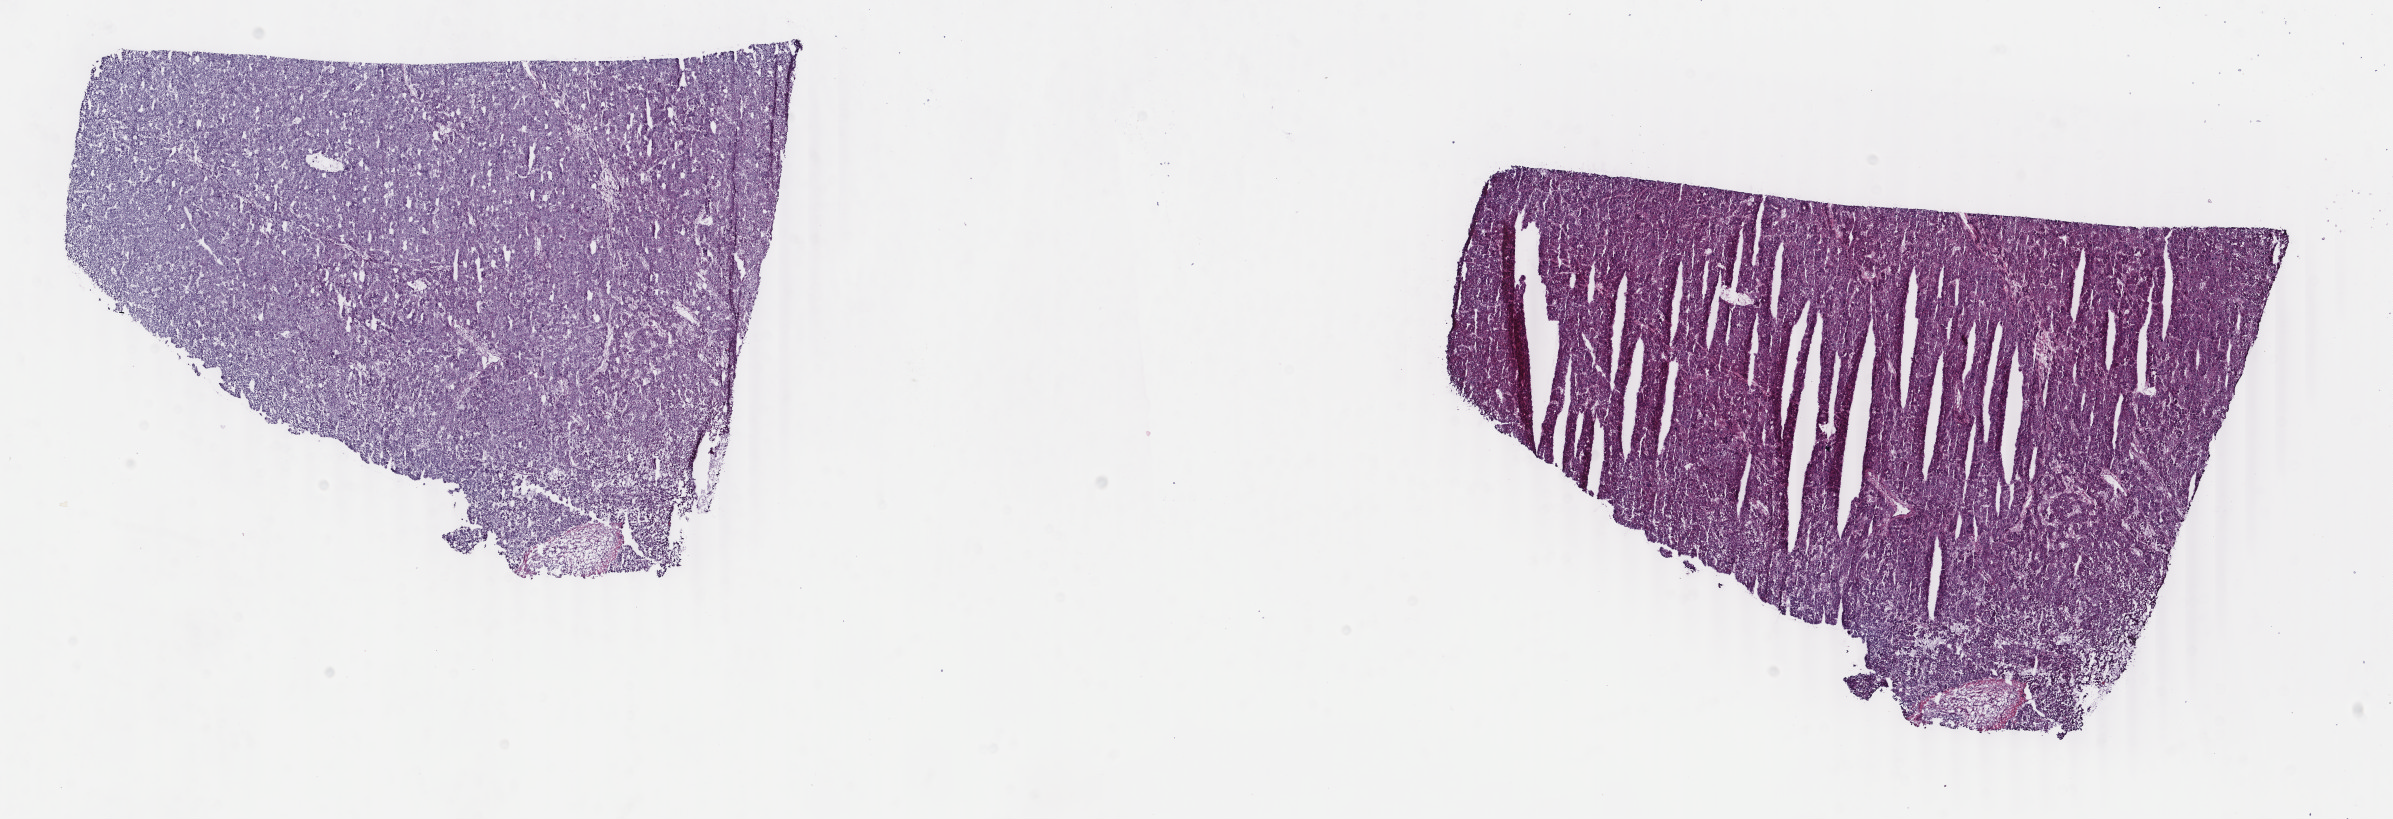
Whole-slide histology image, Hematoxylin and eosin (H&E) stained, low-resolution overview of the scanned area, about 19.0 x 6.5 mm (acquisition: 40x scan), frozen section, sample: primary tumour, liver. Male patient; age at initial diagnosis 67 years. Histologic grade: G3 (poorly differentiated). Composition of this section per pathologist review: tumour cells 90%, tumour nuclei 90%, normal cells 0%, stromal cells 10%, necrosis 0%. Infiltration values recorded for this section: lymphocyte infiltration 2%, monocyte infiltration 0%, neutrophil infiltration 0%.
- AJCC pathologic stage: I (6th edition)
- histologic diagnosis: Hepatocellular carcinoma, NOS